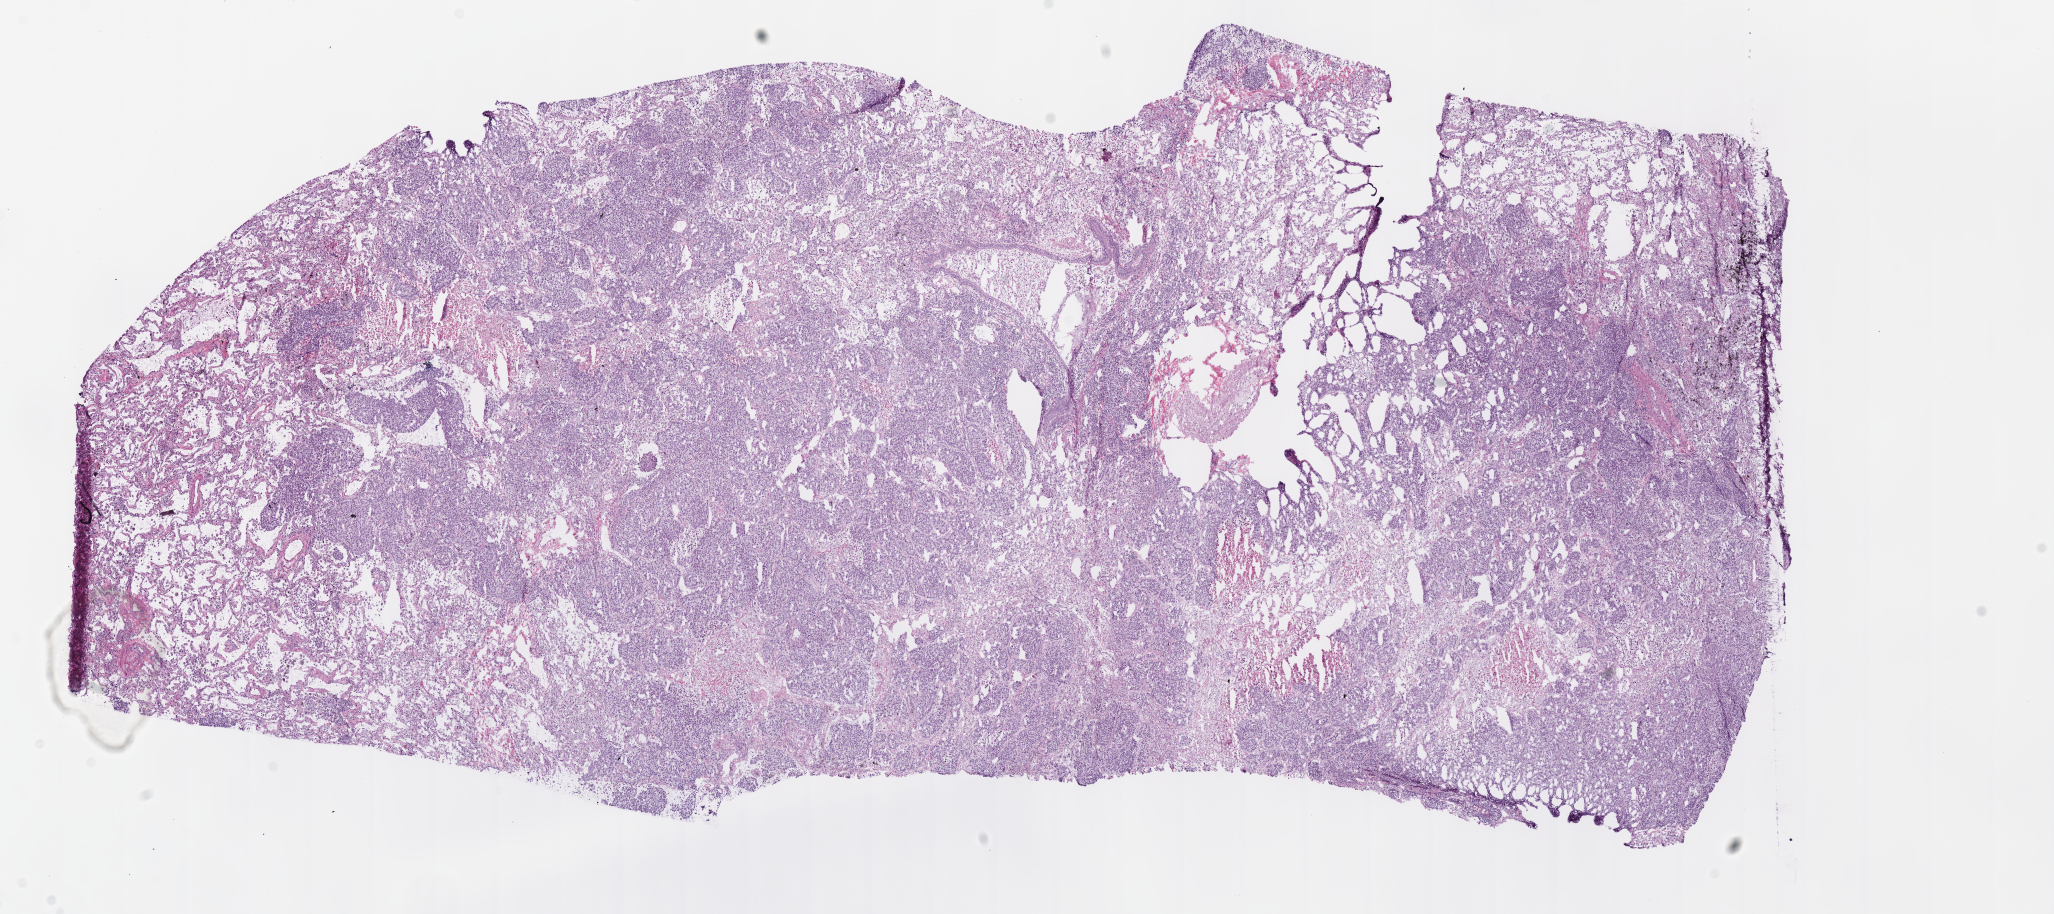
Whole-slide histology image, H&E-stained — a low-resolution overview of the entire scanned area, about 16.2 x 7.2 mm (slide scanned at 40x); frozen section; lung, primary tumour sample. Male patient; age at initial diagnosis 59 years. Pathologist review of this section (percent, as recorded): tumour cells 65%, tumour nuclei 70%, normal cells 20%, stromal cells 10%, necrosis 5%.
AJCC pathologic stage: IIA (7th edition). Laterality: right. Pathologic diagnosis: Adenocarcinoma, NOS.